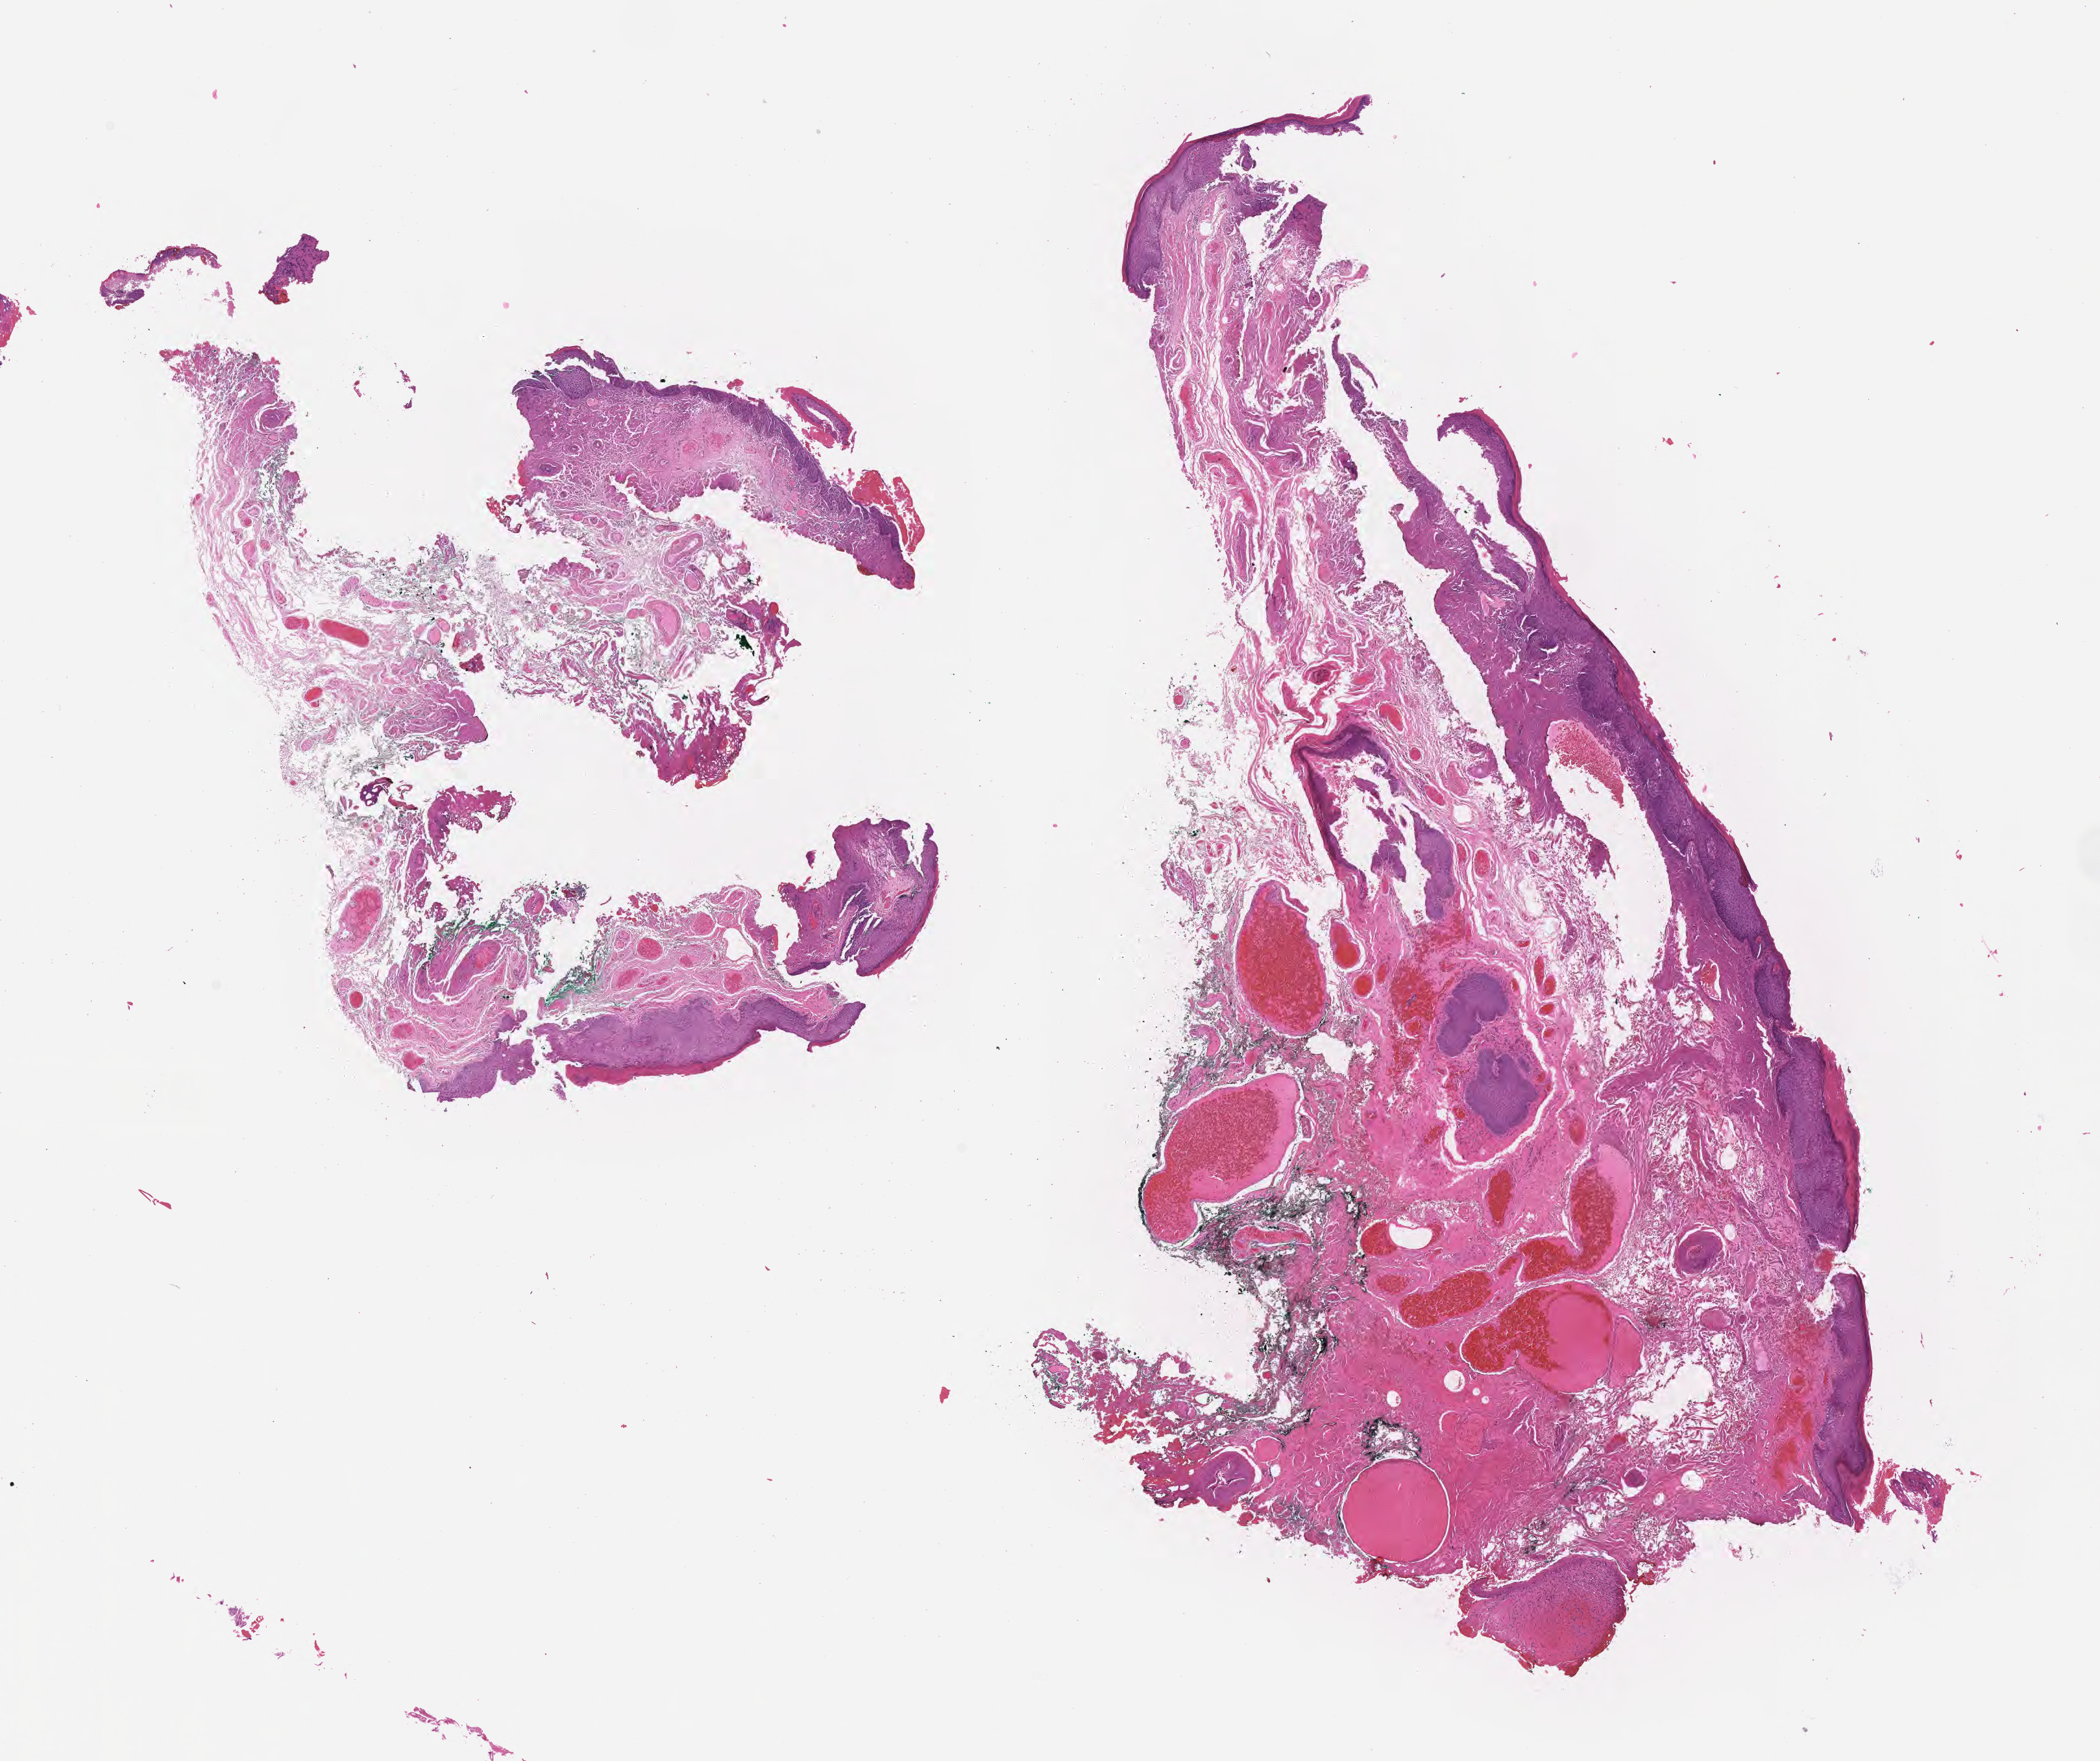
Hematoxylin and eosin (H&E) whole-slide image — shown as a low-resolution overview of the whole scanned area (about 13.1 x 11.0 mm). Formalin-fixed paraffin-embedded section. Non-tumor (normal tissue) sample from a patient with burkitt lymphoma, NOS. Male patient, aged 46. Pathologist review of this section (percent, as recorded): tumor cells 0%, tumor nuclei 0%, stromal cells 0%, necrosis 0%, normal cells 100%. Infiltration values recorded for this section: lymphocyte infiltration 60%, monocyte infiltration 20%, neutrophil infiltration 10%.
This section: non-tumor tissue sample; the patient's diagnosis is given above. Section: top of the tissue portion.